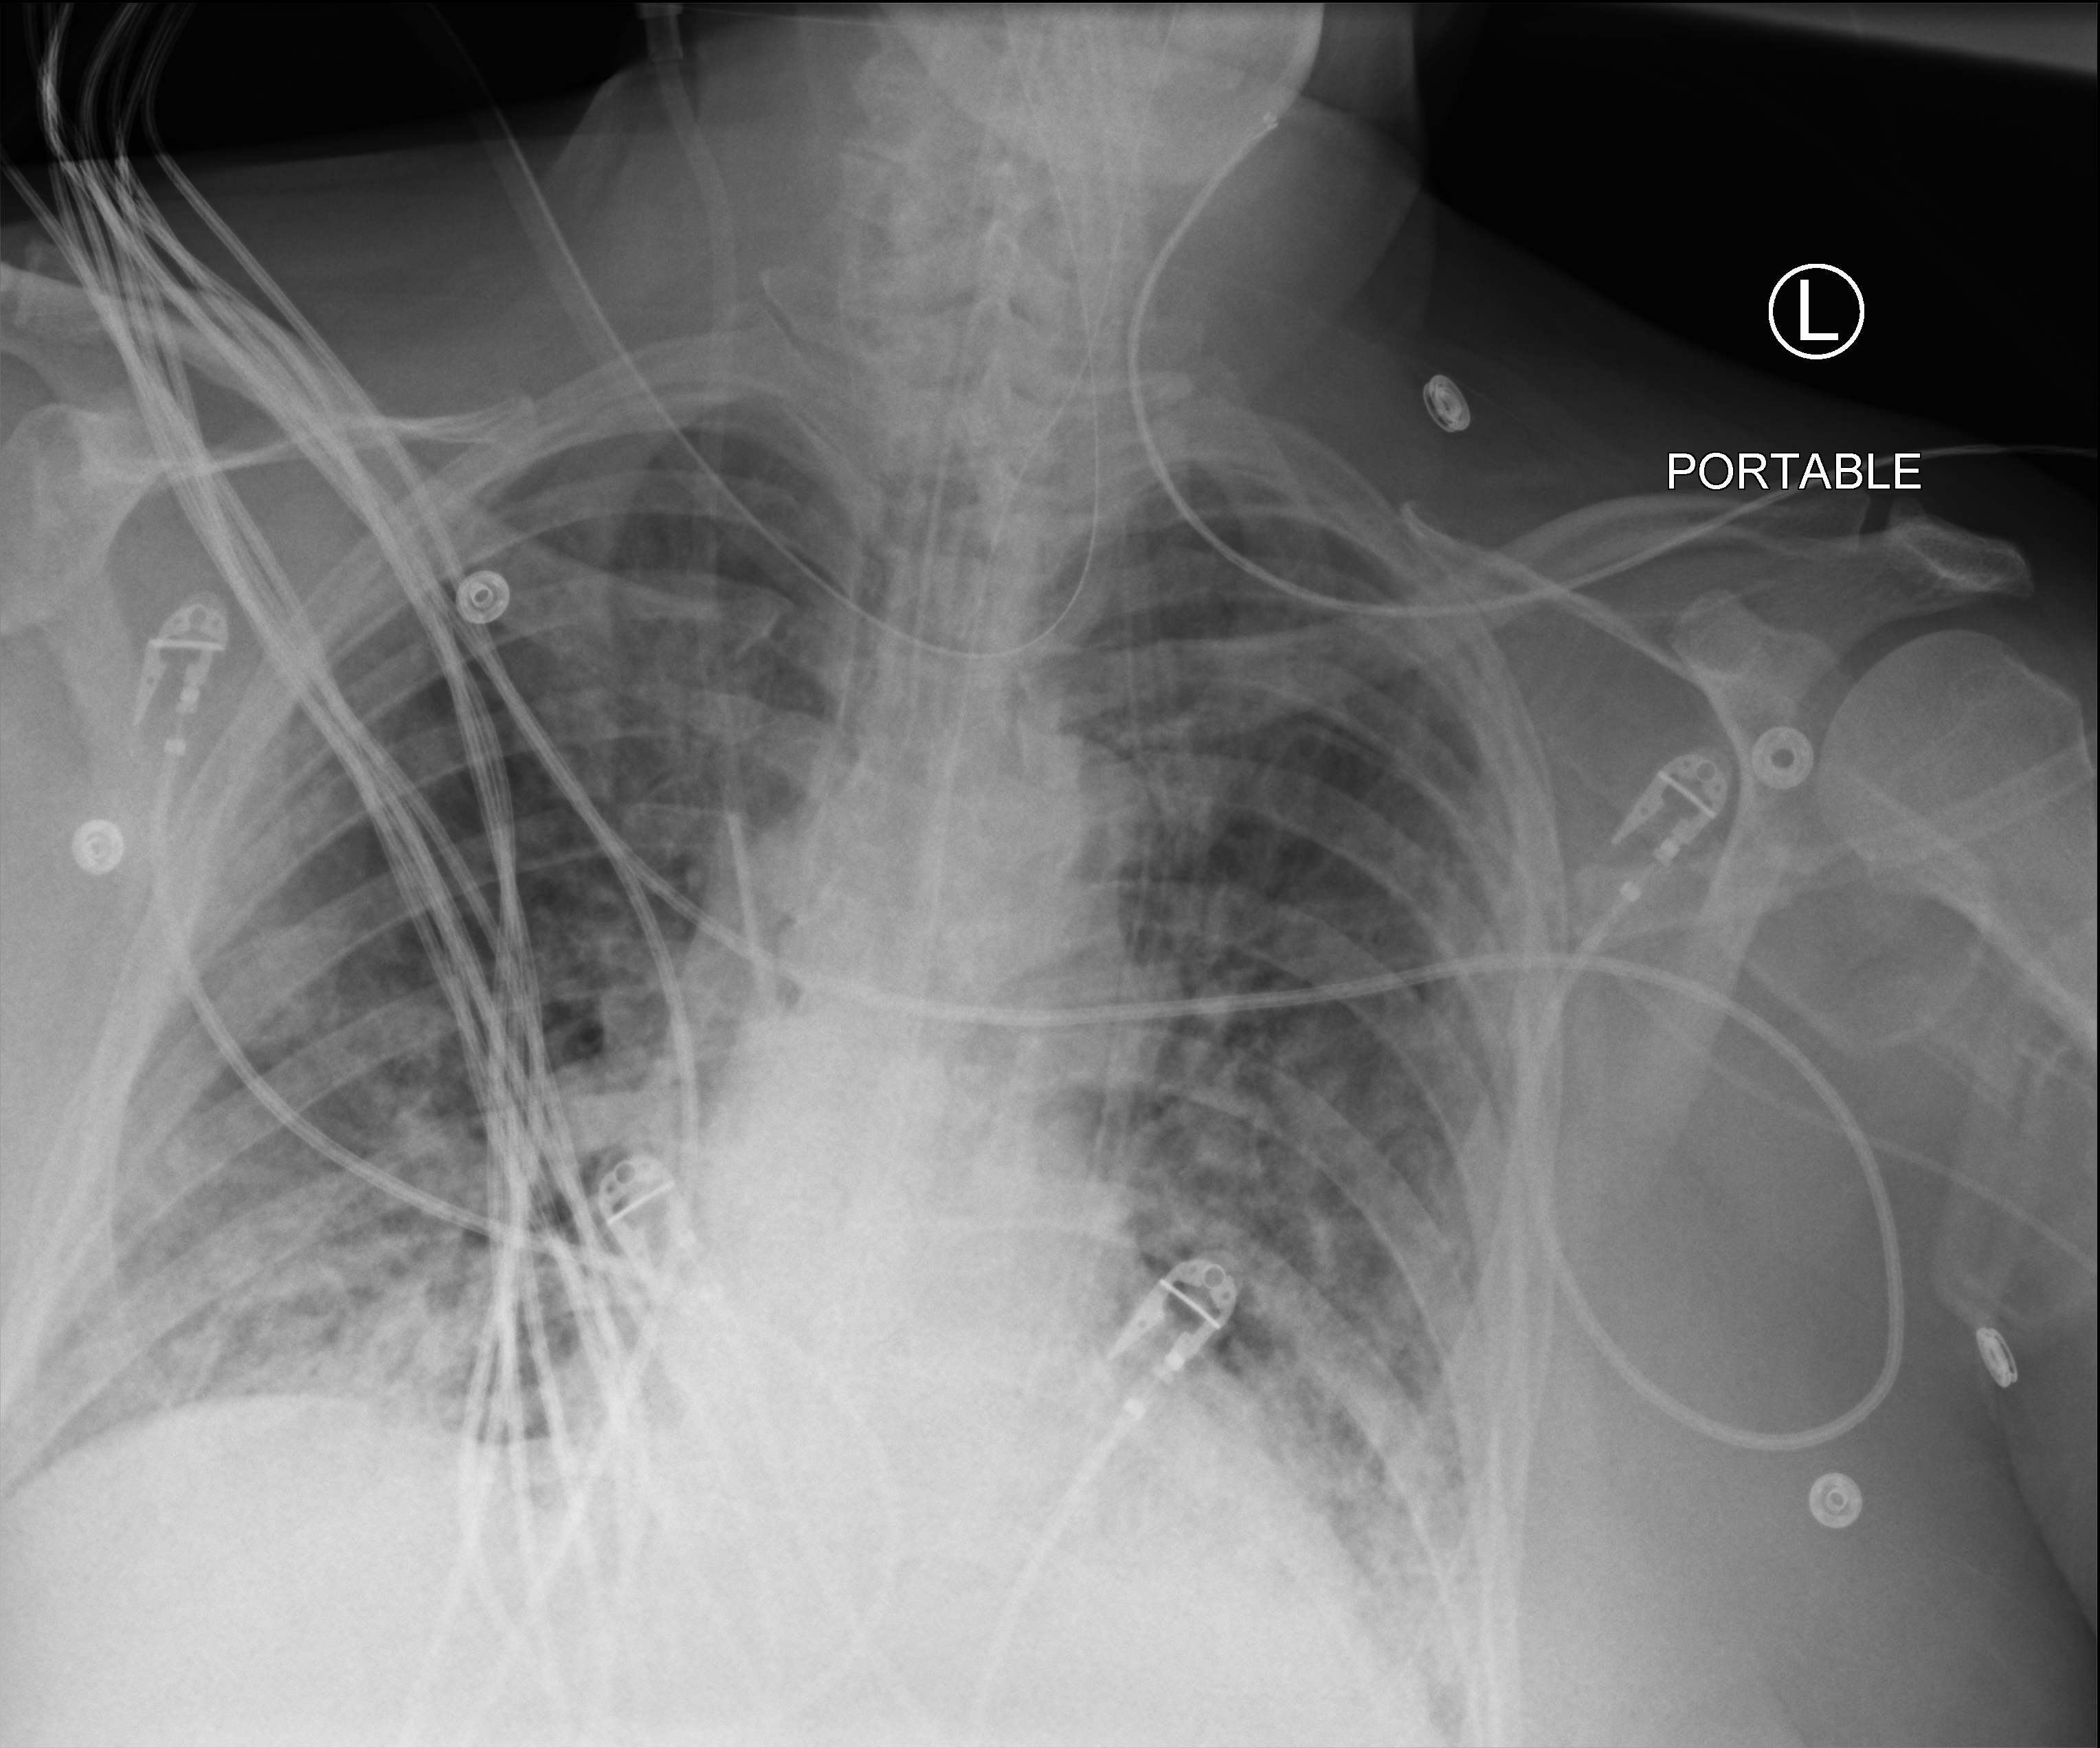
Portable chest radiograph. Patient hospitalised with COVID-19; male, aged 60–74 years.
Admission-level facts for this patient (not findings on this image; timing relative to this image not recorded): COPD (admission record): no; admitted to intensive care during this hospital stay: yes.